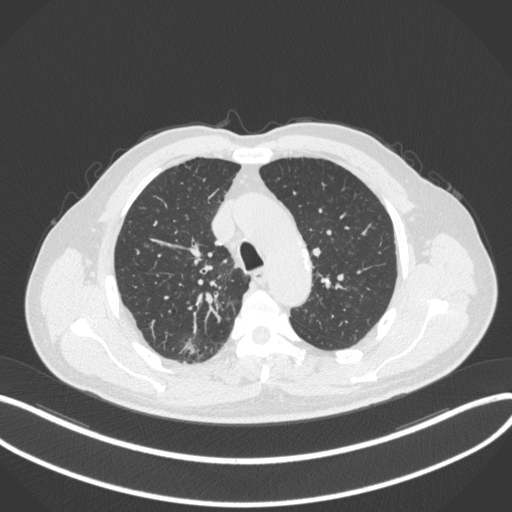
Chest CT, one axial slice; slice 276 of 366 in the series (ordered by position); reconstruction kernel B31f; 120 kVp; lung window (W 1500 / L -600 HU); 1 mm slice thickness; 512 × 512 image matrix. Patient: male, 69 years. From the clinical record (not read from this slice): clinical TNM (as recorded): T1b N0 M0; histopathological grade: G2-3.
Annotated regions visible in this slice (bounding box drawn by a radiologist):
- lung tumour (recorded histology: adenocarcinoma): box from (x=179, y=333) to (x=203, y=360) px